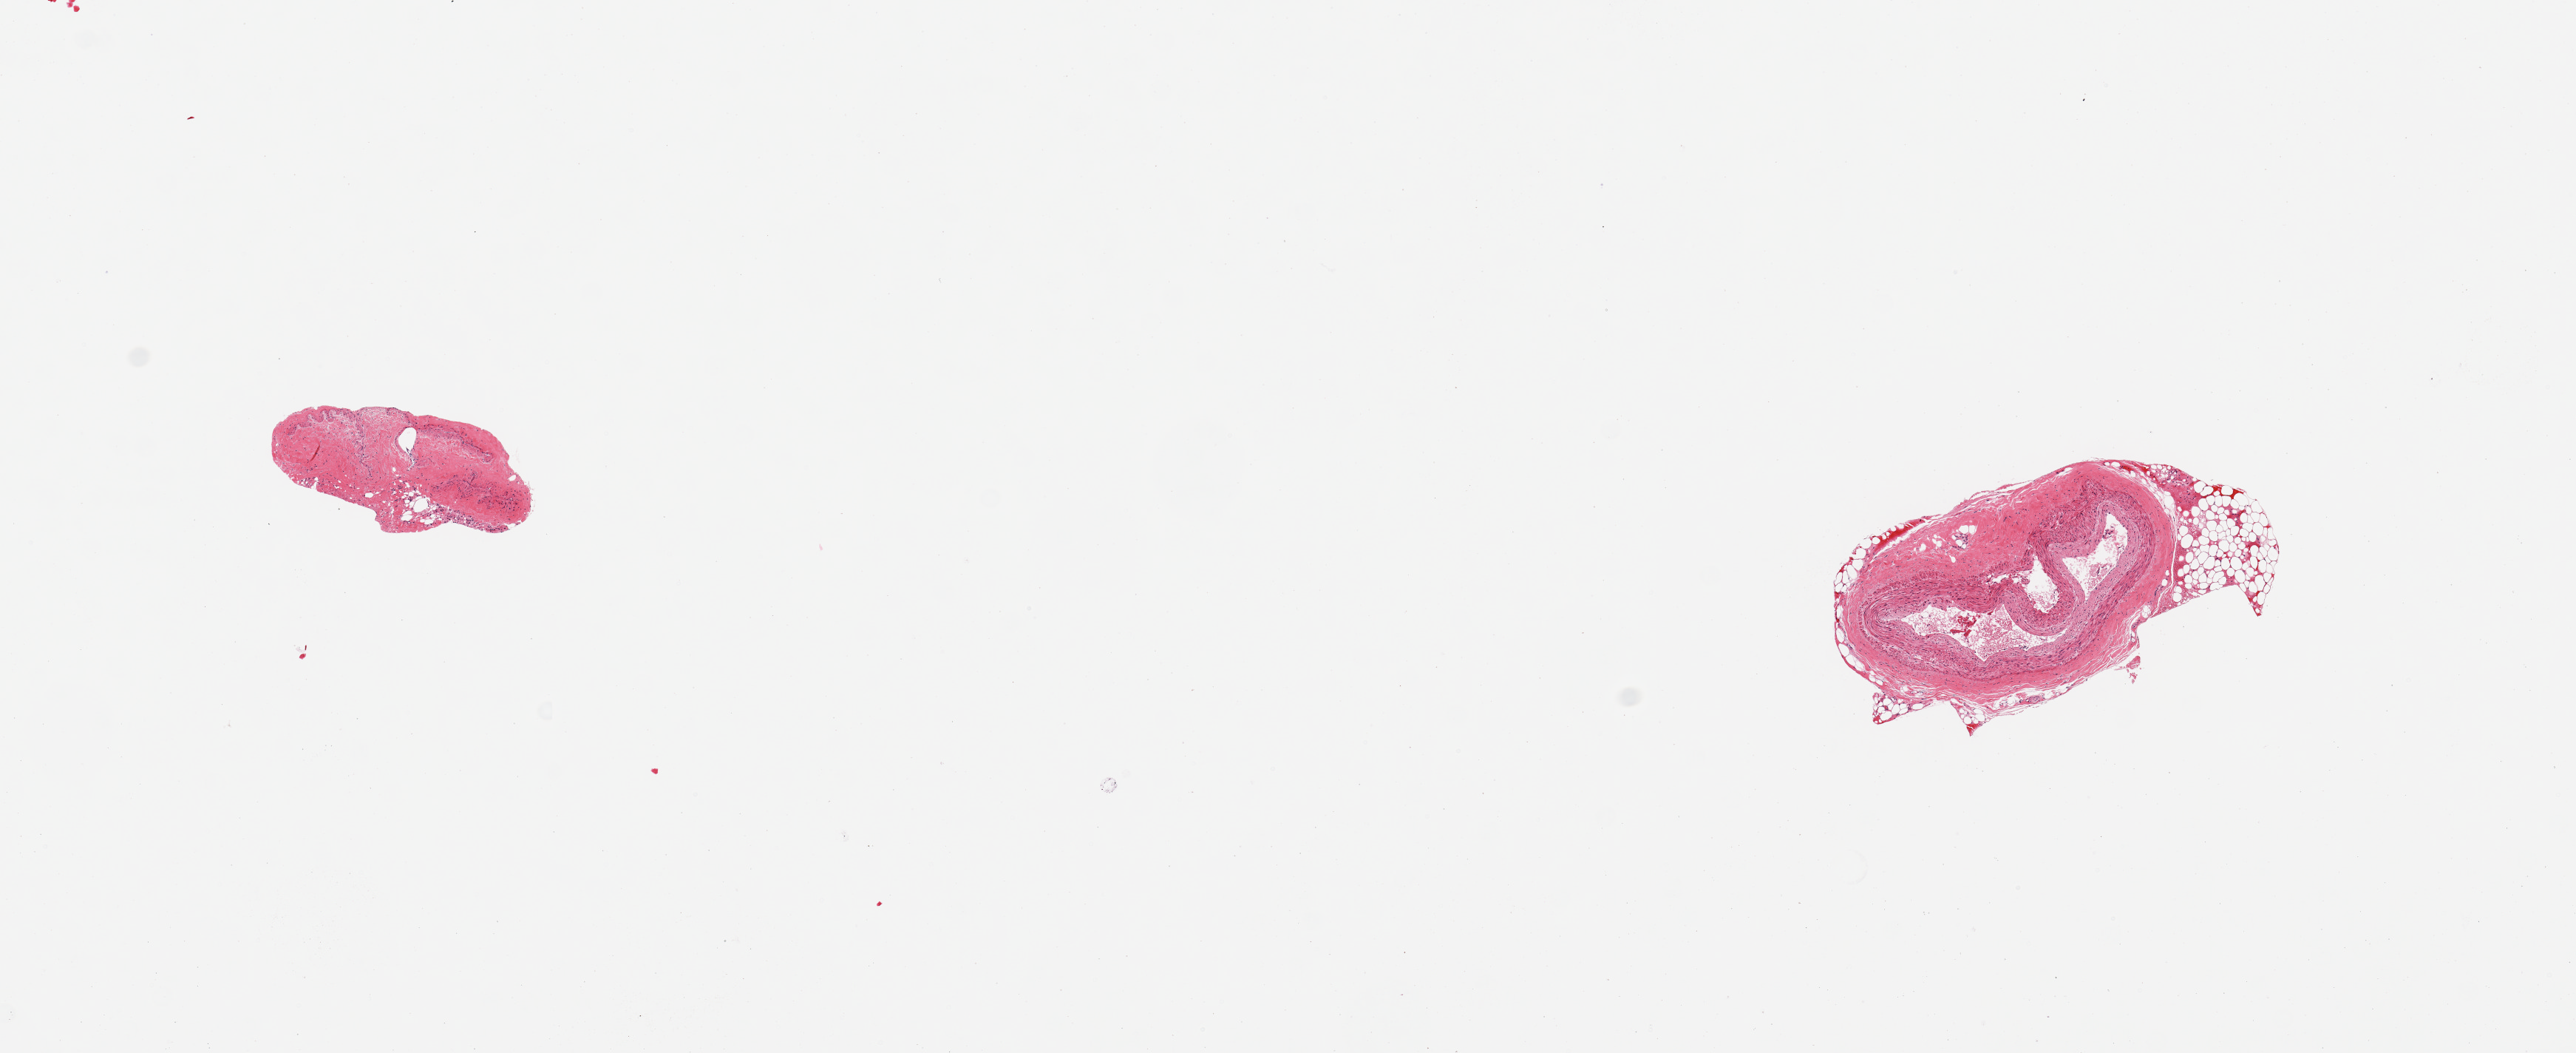
Digitized H&E-stained section, a low-resolution overview of the entire scanned area, about 13.8 x 5.6 mm (slide scanned at 20x). PAXgene-fixed, paraffin-embedded tissue. Section of coronary artery (target tissue). Tissue donor sample. Donor: female.
- review note (as recorded): 2 pieces, one with adherent fat up to ~0.6mm